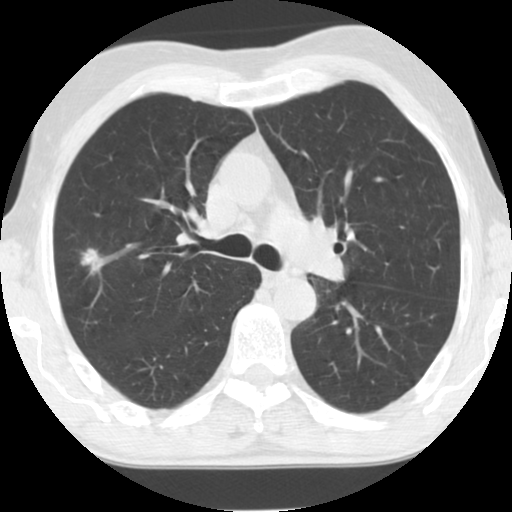
Chest CT (low-dose screening protocol), one axial image; second screening round (one year after baseline); lung window (W 1500 / L -600 HU); standard (soft-tissue) reconstruction kernel (STANDARD); slice 42 of 124 in the series; 512 × 512 image matrix, field of view 310 × 310 mm. Male, age 69 years at enrolment. Former smoker at enrolment.
- Expert reader's lesion annotation, bounding box (x1, y1, x2, y2) in pixels: (67, 237, 121, 288).
- Screening reader's record for this exam (one nodule recorded; not confirmed to be the boxed lesion): non-calcified nodule or mass ≥4 mm, right upper lobe, 12 × 8 mm, spiculated (stellate) margins, soft tissue attenuation, pre-existing on the prior screen: yes; interval growth: yes.
- Official screen result: positive, other.
- Participant outcome: lung cancer diagnosed 196 days after this screen — mucinous adenocarcinoma, right upper lobe, moderately differentiated (G2), stage IA (AJCC 6th edition), 11 mm at pathology.